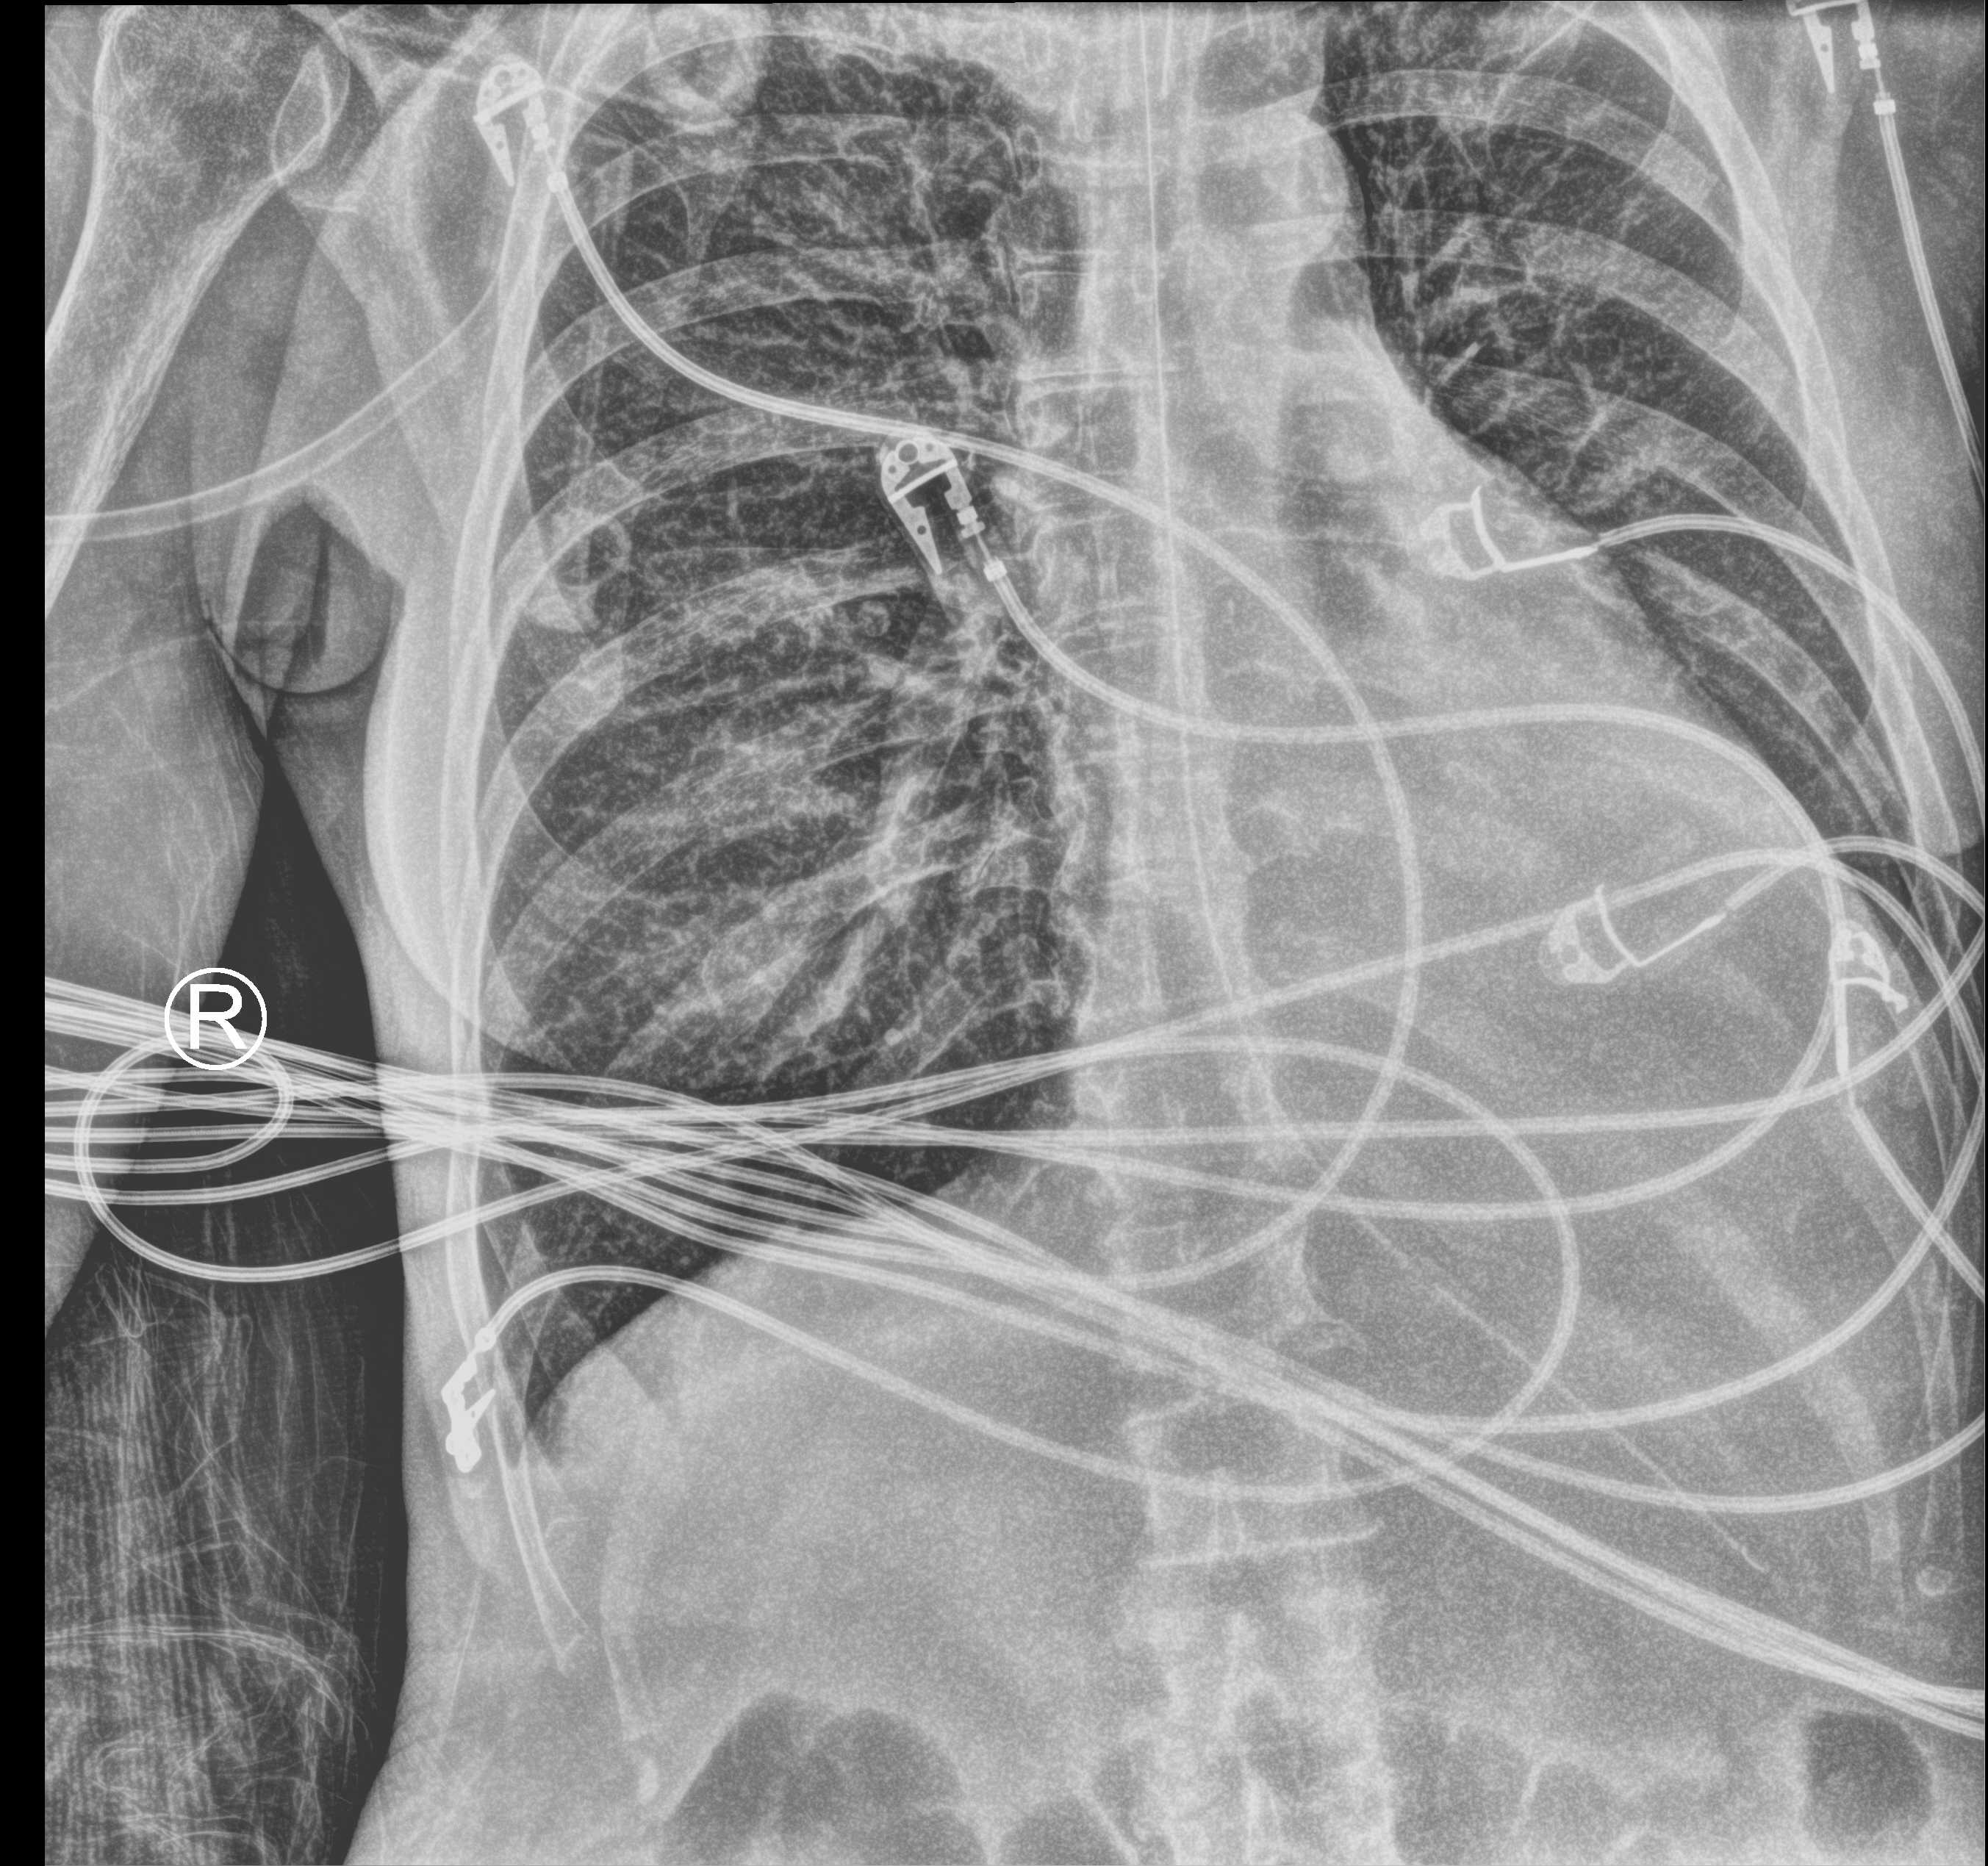
Chest X-ray (portable); anteroposterior (AP) projection. Female patient hospitalised with COVID-19, age 60–74 years.
Hospital-stay facts (about this admission, not read from this image; timing relative to this image not recorded):
- mechanically ventilated during this hospital stay: yes
- admitted to intensive care during this hospital stay: yes